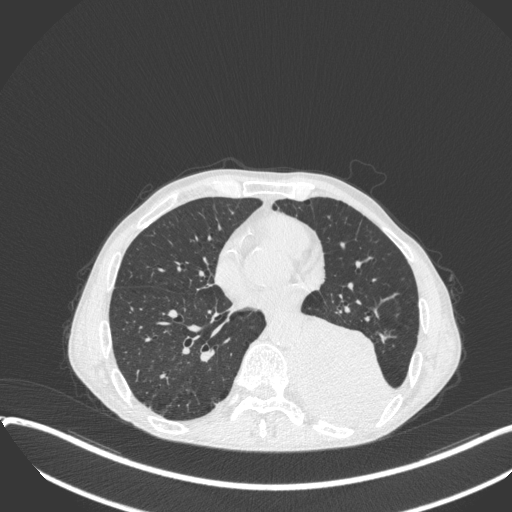
Chest CT, one axial slice. Position 150 of 400 along the scan axis. Reconstruction kernel B31f. 120 kVp. Lung window (W 1500 / L -600 HU). 1 mm slice thickness. 512 × 512 image matrix, field of view 400 × 400 mm. Male patient, age 57 years. From the clinical record (not read from this slice): clinical TNM (as recorded): T4 N0 M0.
Structures marked on this image (bounding box drawn by a radiologist):
- lung tumour (recorded histology: squamous cell carcinoma): box from (x=298, y=306) to (x=398, y=433) px